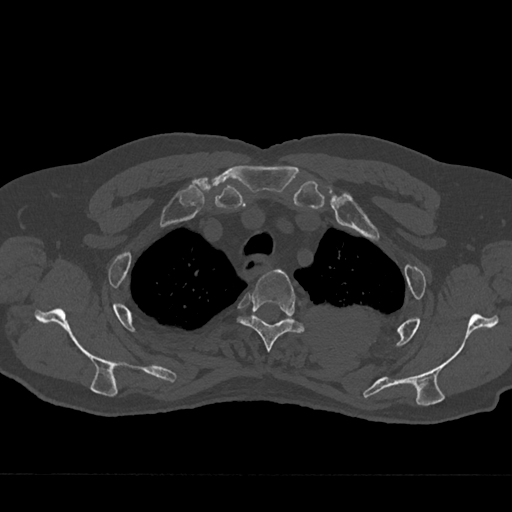
CT including the spine, one axial slice; position 568 of 797 along the scan axis; reconstruction kernel Br40s/3; 120 kVp; bone window (W 1800 / L 400 HU); 512 × 512 image matrix, field of view 377 × 377 mm. Patient: male, 75 years. From the clinical record (not read from this slice): primary cancer: renal; vertebrae with lytic lesions (as recorded): T4.
Structures marked on this image (semi-automatic segmentation, software-assisted and operator-edited):
- T3 vertebra: bounding box (x1, y1, x2, y2) in pixels: (238, 269, 305, 352)